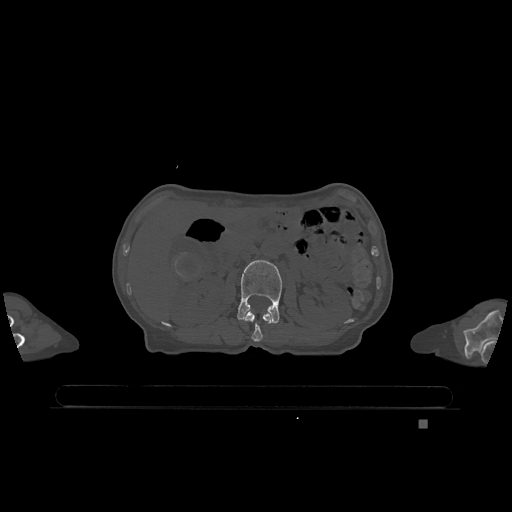
CT including the spine, one axial slice. Slice 435 of 1317 in the series (ordered by position). Bone window (W 1800 / L 400 HU). 0.5 mm slice thickness. 512 × 512 image matrix, field of view 500 × 500 mm. Female patient, age 74 years. From the clinical record (not read from this slice): primary cancer: lung; vertebrae with lytic lesions (as recorded): T1, T4, T5, T6, L4, L5.
Outlined on this slice (semi-automatic segmentation, software-assisted and operator-edited):
- L1 vertebra: bounding box <244,310,272,342> (left, top, right, bottom; pixels)
- L2 vertebra: <237,260,282,323>